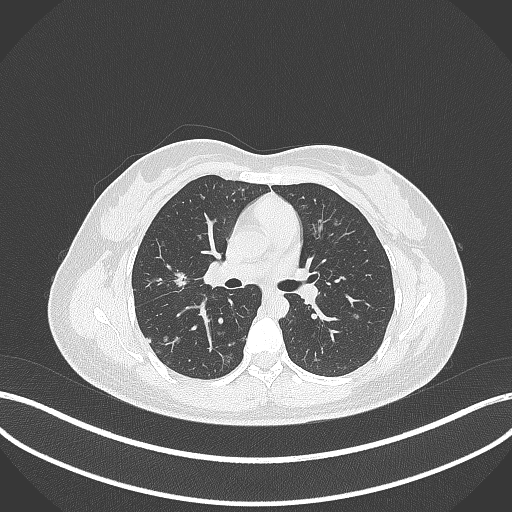
Chest CT, one axial slice; position 195 of 307 along the scan axis; reconstruction kernel B70f; lung window (W 1500 / L -600 HU); 512 × 512 image matrix, field of view 400 × 400 mm. Female patient, age 33 years. From the clinical record (not read from this slice): clinical TNM (as recorded): T1c N0 M0; histopathological grade: G2-G3.
Outlined on this slice (rectangle marked by the reading radiologist):
- lung tumour (recorded histology: adenocarcinoma): bounding box <168,267,192,293> (left, top, right, bottom; pixels)